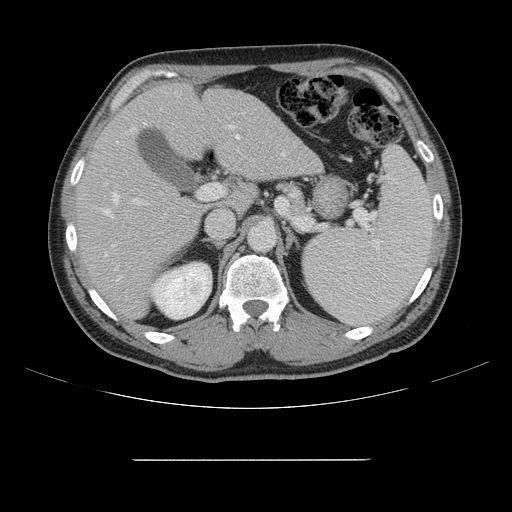
Contrast-enhanced abdominal CT, one axial slice; slice 94 of 164 in the series (ordered by position); 120 kVp; intravenous contrast given; soft-tissue window (W 400 / L 40 HU); 2.5 mm slice thickness; 512 × 512 image matrix, field of view 404 × 404 mm. Male patient, age 54 years. Case-level facts recorded for this patient, not image findings: diagnosis: colorectal cancer liver metastases, imaged before liver resection; multiple liver metastases: yes; largest metastasis: 1 cm; disease in both lobes: no.
Outlined on this slice (expert manual segmentation):
- hepatic veins: bounding box <104,134,285,281> (left, top, right, bottom; pixels)
- liver: <78,83,320,319>
- planned liver remnant (the part of the liver to remain after resection): <77,83,233,318>
- portal vein (with intrahepatic branches): <132,92,240,203>